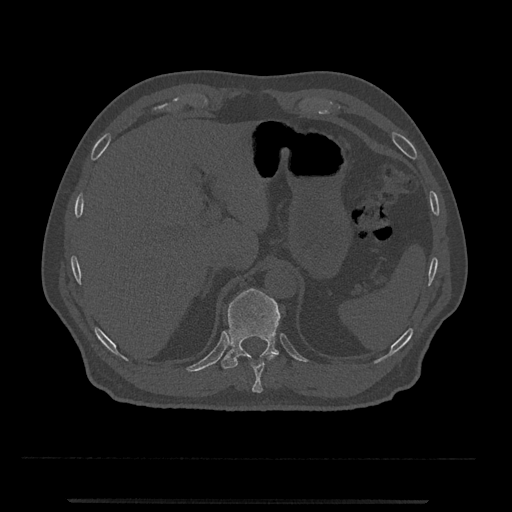
CT including the spine, one axial slice. 120 kVp. Bone window (W 1800 / L 400 HU). 0.5 mm slice thickness. 512 × 512 image matrix, field of view 419 × 419 mm. Male patient, age 63 years. Case-level facts recorded for this patient, not image findings: primary cancer: prostate.
Annotated regions visible in this slice (semi-automatic segmentation, software-assisted and operator-edited):
- T10 vertebra: bounding box <251,354,276,393> (left, top, right, bottom; pixels)
- T11 vertebra: <220,288,280,369>